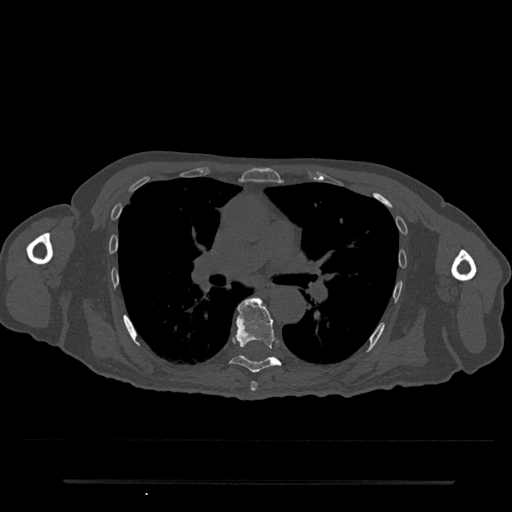
CT including the spine, one axial slice. Slice 483 of 797 in the series (ordered by position). 120 kVp. Bone window (W 1800 / L 400 HU). 512 × 512 image matrix, field of view 427 × 427 mm. Patient: male, 74 years. Case-level facts recorded for this patient, not image findings: primary cancer: prostate.
Annotated regions visible in this slice (semi-automatically segmented with operator editing):
- T6 vertebra: bounding box [x1, y1, x2, y2] px = [250, 382, 258, 392]
- T7 vertebra: [230, 297, 282, 373]